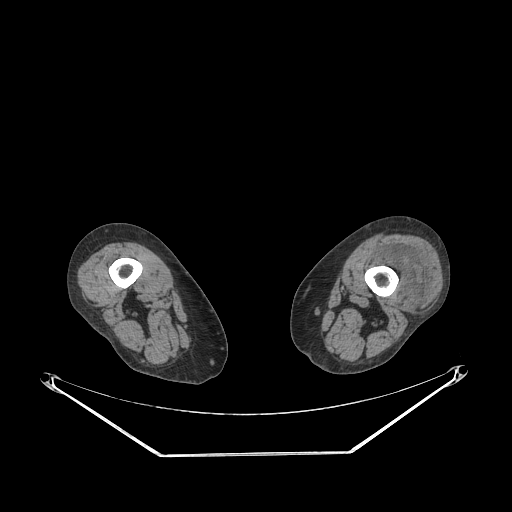
CT of an extremity soft-tissue mass (from a PET/CT study), one axial slice; 140 kVp; soft-tissue window (W 400 / L 40 HU); 3.75 mm slice thickness; 512 × 512 image matrix, field of view 500 × 500 mm. Female patient. Case-level facts recorded for this patient, not image findings: histological type: undifferentiated – high grade; grade: high; site of the primary tumour: left thigh.
Outlined on this slice (expert contour drawn on MRI and transferred to this co-registered scan by the dataset authors):
- gross tumour volume including surrounding oedema: bounding box (x1, y1, x2, y2) in pixels: (372, 246, 432, 307)